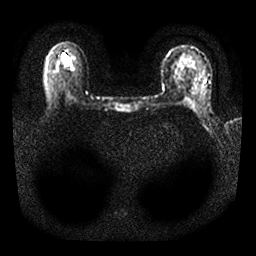
Breast MRI, one axial slice. Slice 18 of 25 in the series (ordered by position). Diffusion-weighted series; image 2 of 4 stored at this slice position (different b-values; order by instance number). 1.5 T. 4 mm slice thickness. 256 × 256 image matrix, field of view 310 × 310 mm. Female patient.
Annotated regions visible in this slice (manually delineated by an expert):
- tumour on diffusion-weighted imaging: bounding box (x1, y1, x2, y2) in pixels: (61, 58, 68, 62)